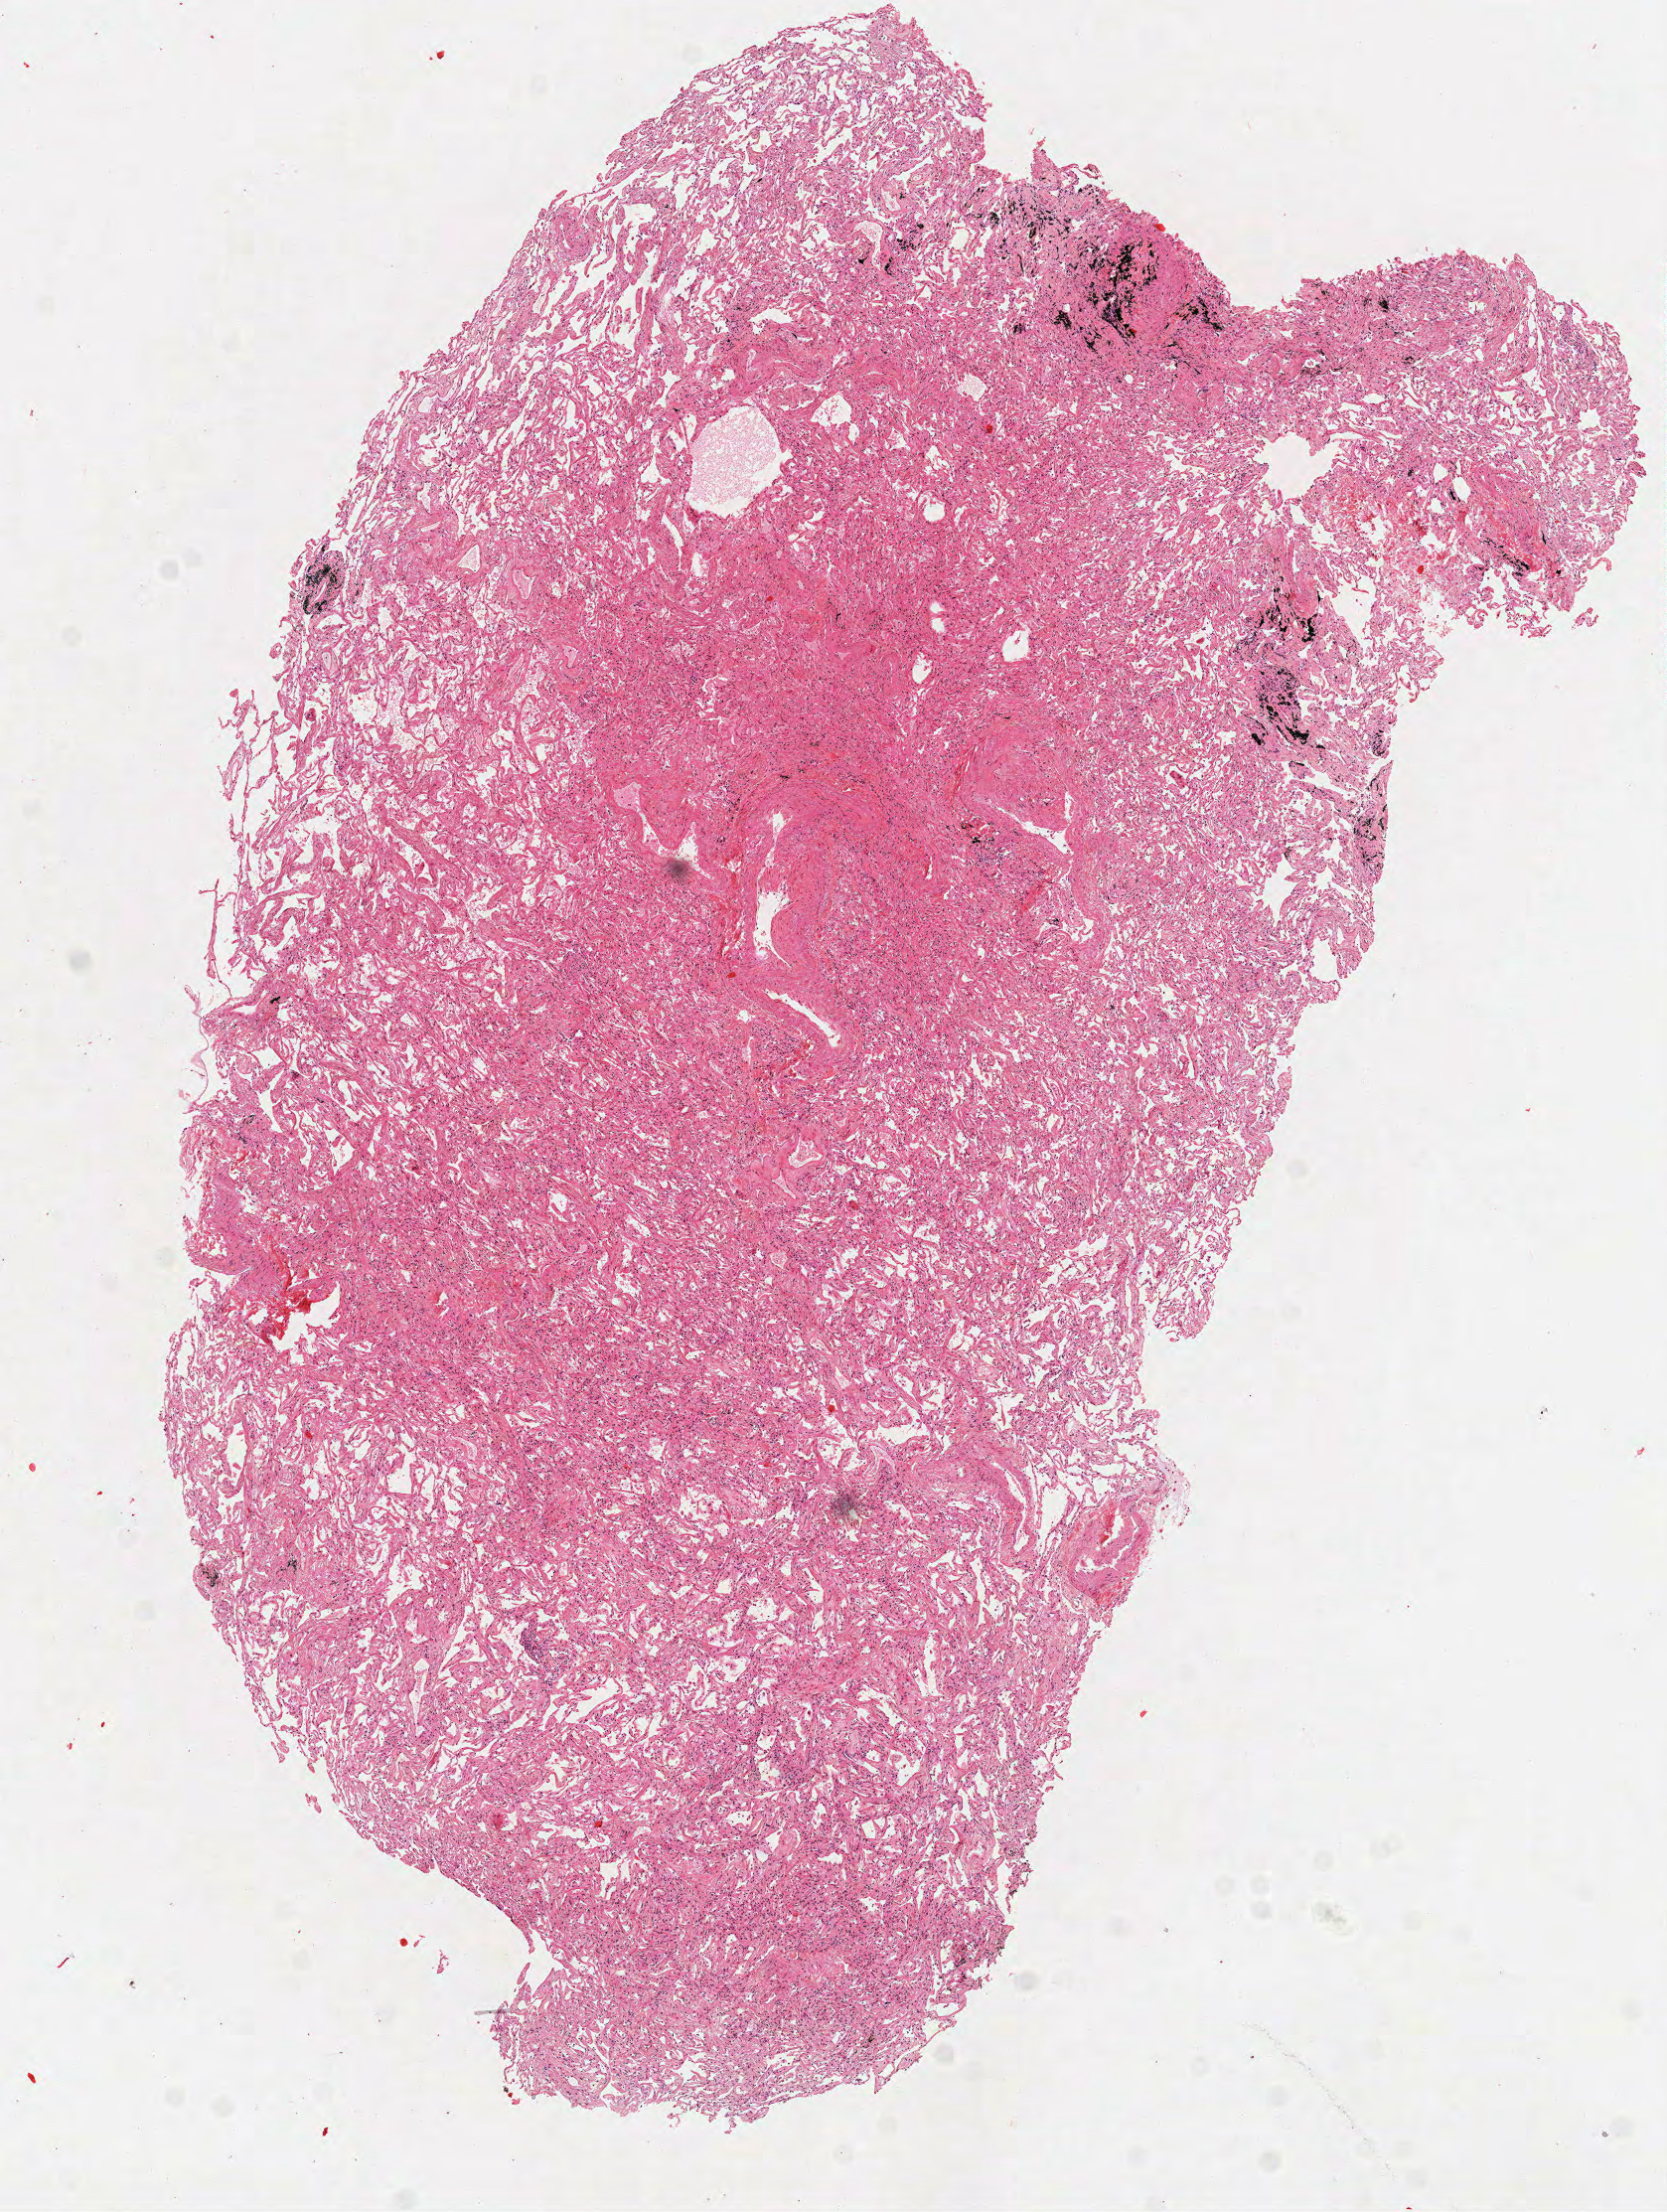
Digitized H&E tissue section (whole slide), low-resolution overview of the scanned area, about 6.8 x 9.0 mm (acquisition: 40x scan). Frozen section. Solid tissue normal (non-tumour tissue) sample from the lung. Patient: male, age at initial diagnosis 64 years.
• this section: solid tissue normal (non-tumour) sample from the same patient
• patient diagnosis: Squamous cell carcinoma, NOS (upper lobe, lung)